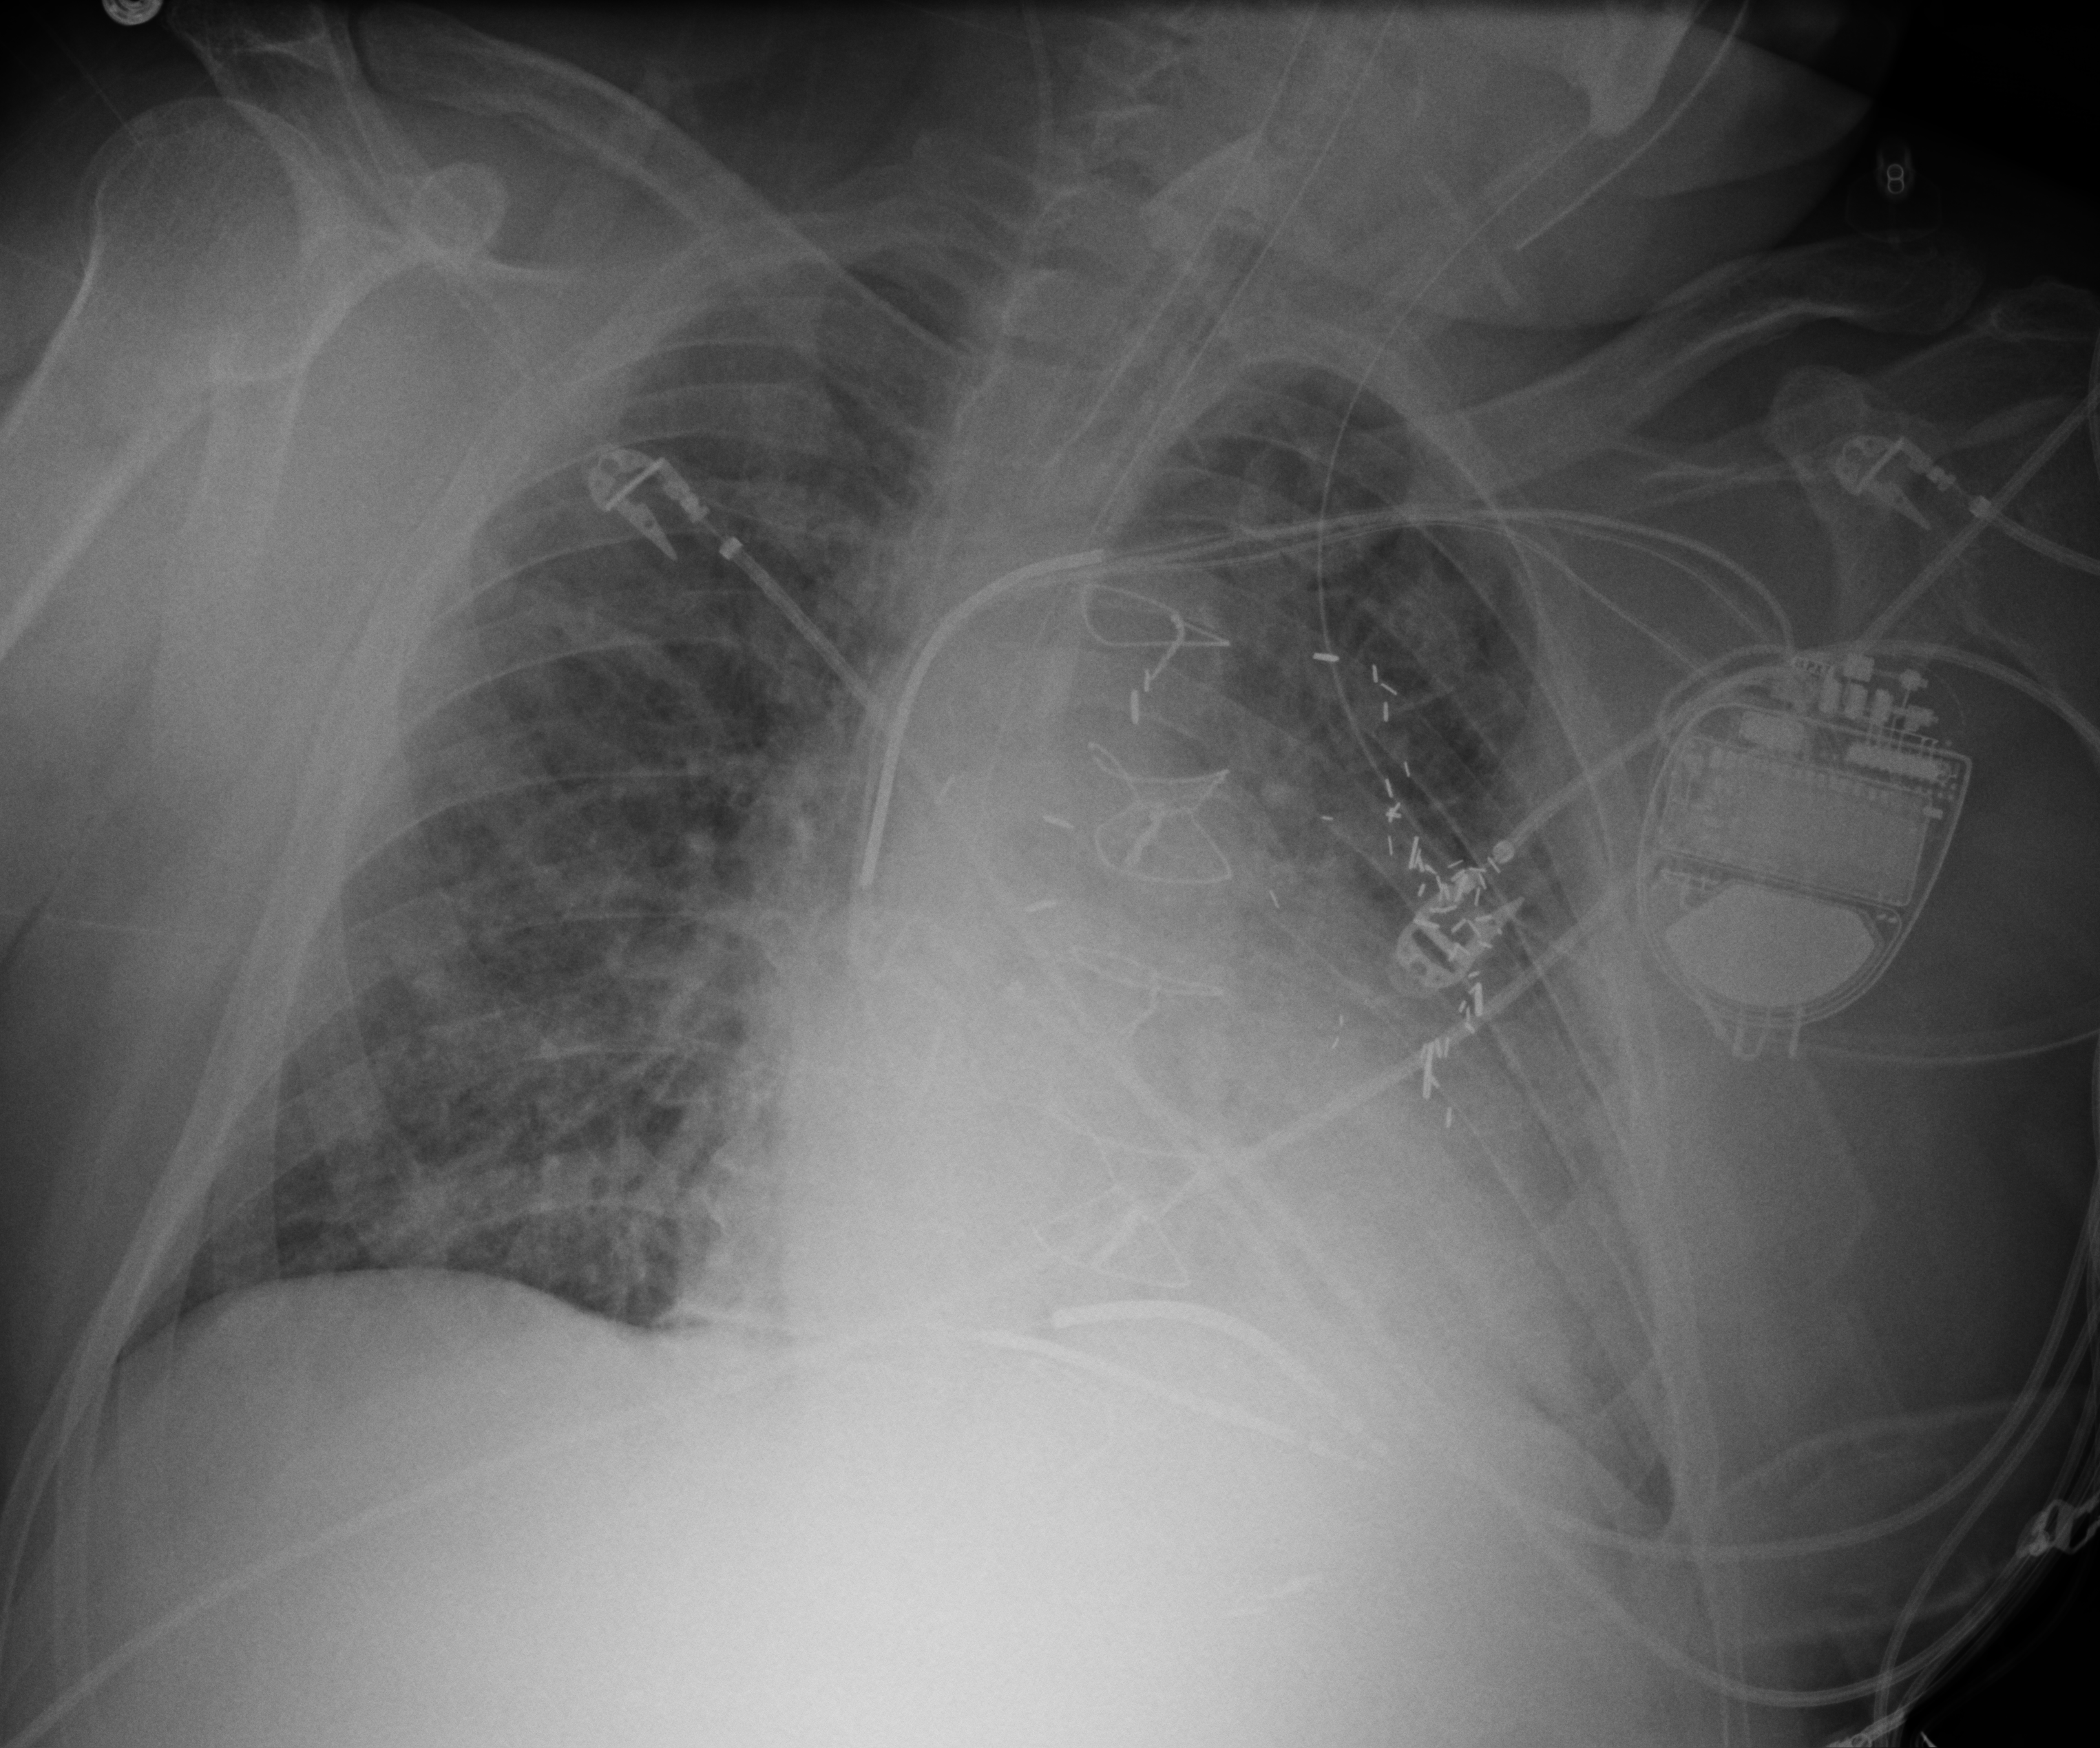
Bedside chest radiograph (computed radiography); anteroposterior (AP) projection. Male patient hospitalised with COVID-19, age 60–74 years.
Admission-level facts for this patient (not findings on this image; timing relative to this image not recorded): mechanically ventilated during this hospital stay: yes; admitted to intensive care during this hospital stay: yes.